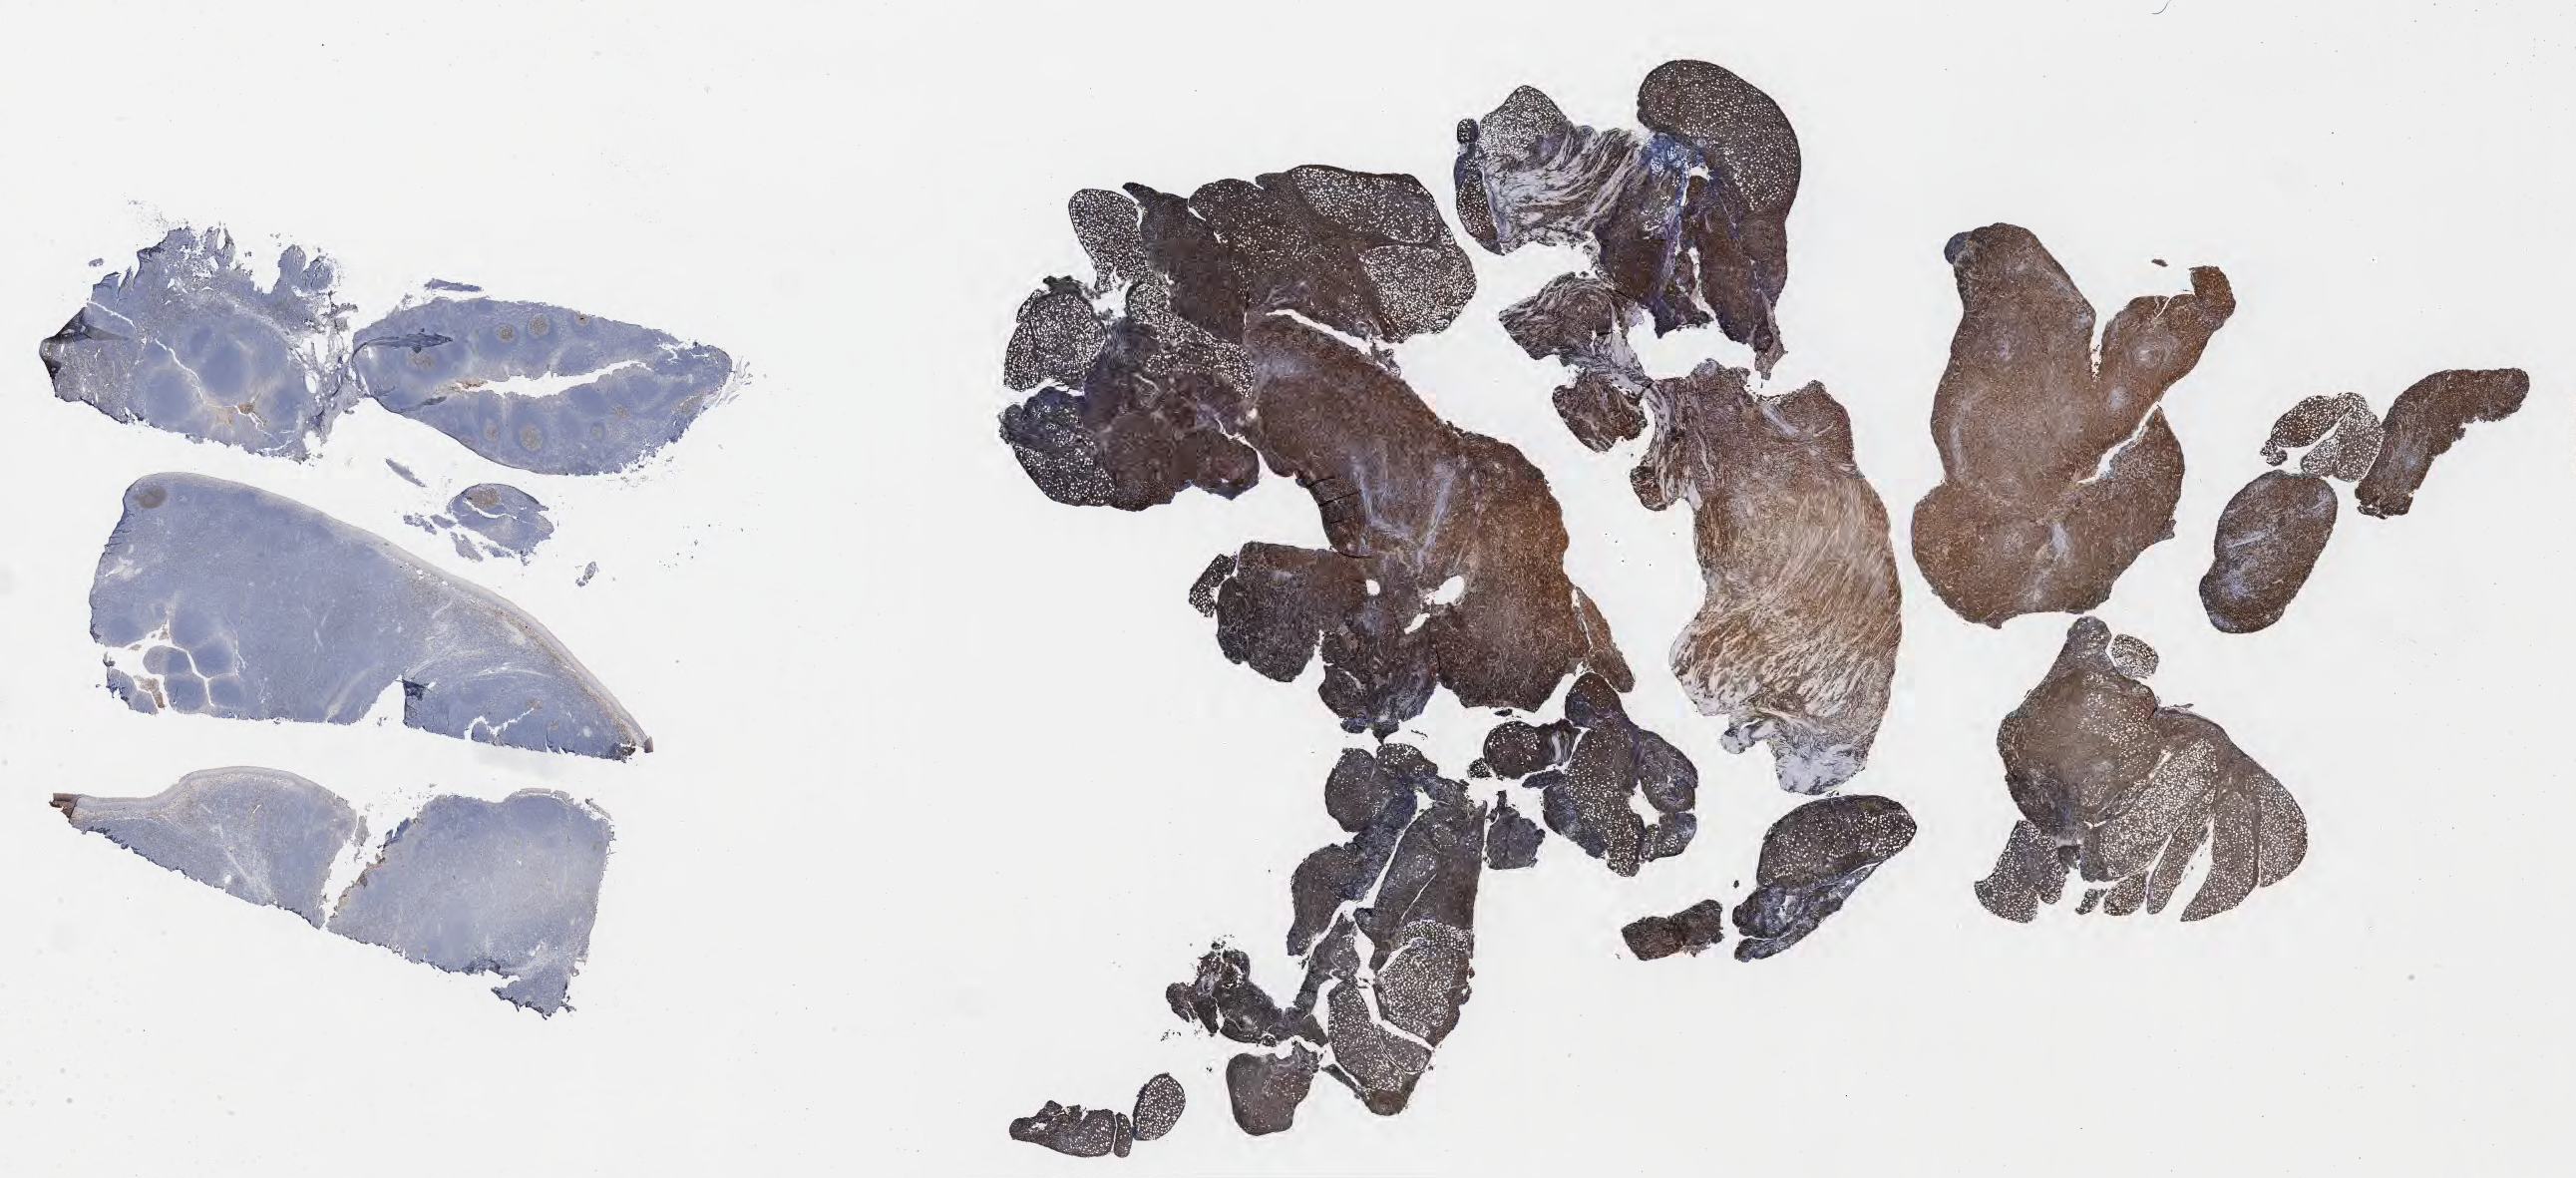
Immunohistochemistry (IHC) whole-slide image stained for CD10 — a low-resolution overview of the entire scanned area, about 41.7 x 19.1 mm; specimen: tumor tissue; anatomic site: abdomen proper. Male patient; age at initial diagnosis 4 years.
Diagnosis: Burkitt lymphoma, NOS.